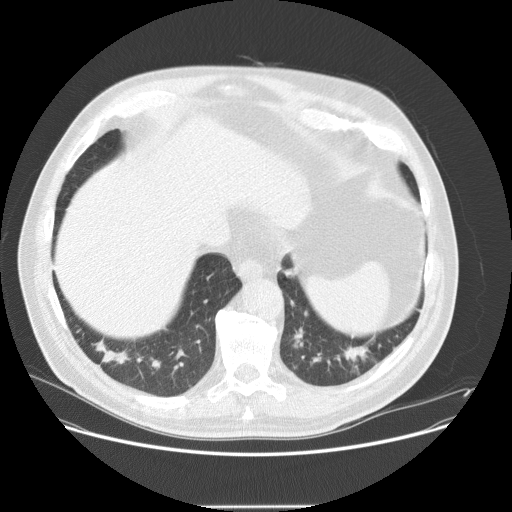
Low-dose screening chest CT, axial slice. First (baseline) screen. Lung window (W 1500 / L -600 HU). Standard (soft-tissue) reconstruction kernel (STANDARD). Male, age 61 years at enrolment. Current smoker at enrolment.
Expert reader's lesion annotation, bounding box <90,333,143,384> (left, top, right, bottom; pixels). The screening reader recorded 2 non-calcified nodules or masses ≥4 mm on this exam (left lower lobe, right lower lobe); which of them this box marks is not recorded. Later outcome: lung cancer diagnosed 41 days after this screen — bronchiolo-alveolar carcinoma, mucinous, right lower lobe, well differentiated (G1), stage IV (AJCC 6th edition), 23 mm at pathology.